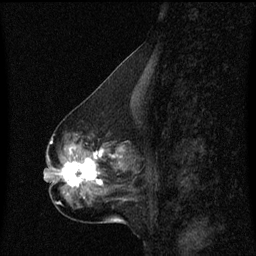
Breast MRI (dynamic contrast-enhanced), one sagittal slice; position 26 of 60 along the scan axis; dynamic contrast-enhanced series, image 2 of 3 at this slice position (ordered by acquisition); 1.5 T; TE 4.2 ms, TR 8.4 ms; 2 mm slice thickness; 256 × 256 image matrix, field of view 200 × 200 mm. Patient: female, 50 years. From the clinical record (not read from this slice): setting: breast cancer imaged before/during neoadjuvant chemotherapy; receptor status: HR-positive, HER2-negative.
Annotated regions visible in this slice (semi-automatically segmented with operator editing):
- analysis volume of interest (the breast-tissue region the enhancement analysis was run in; not a lesion): bounding box (x1, y1, x2, y2) in pixels: (55, 140, 133, 191)
- tumour enhancement mask (voxels above the 70 % enhancement threshold inside the analysis volume of interest): (63, 148, 123, 187)